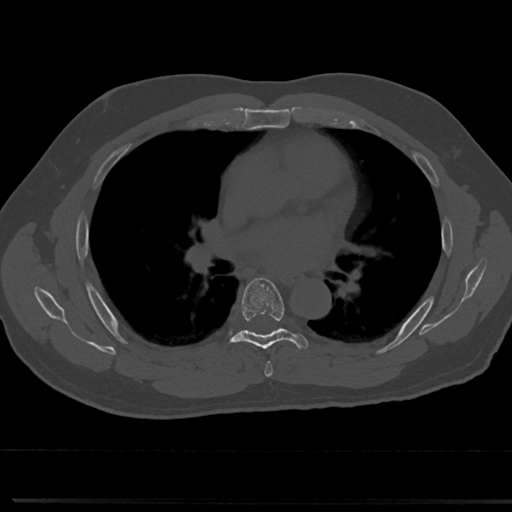
CT including the spine, one axial slice. Reconstruction kernel Br40s/3. Bone window (W 1800 / L 400 HU). 0.5 mm slice thickness. 512 × 512 image matrix, field of view 355 × 355 mm. Male patient, age 61 years. Case-level facts recorded for this patient, not image findings: primary cancer: prostate.
Outlined on this slice (semi-automatic segmentation, software-assisted and operator-edited):
- T5 vertebra: box from (x=261, y=345) to (x=272, y=373) px
- T6 vertebra: (x=218, y=276)–(x=310, y=355)